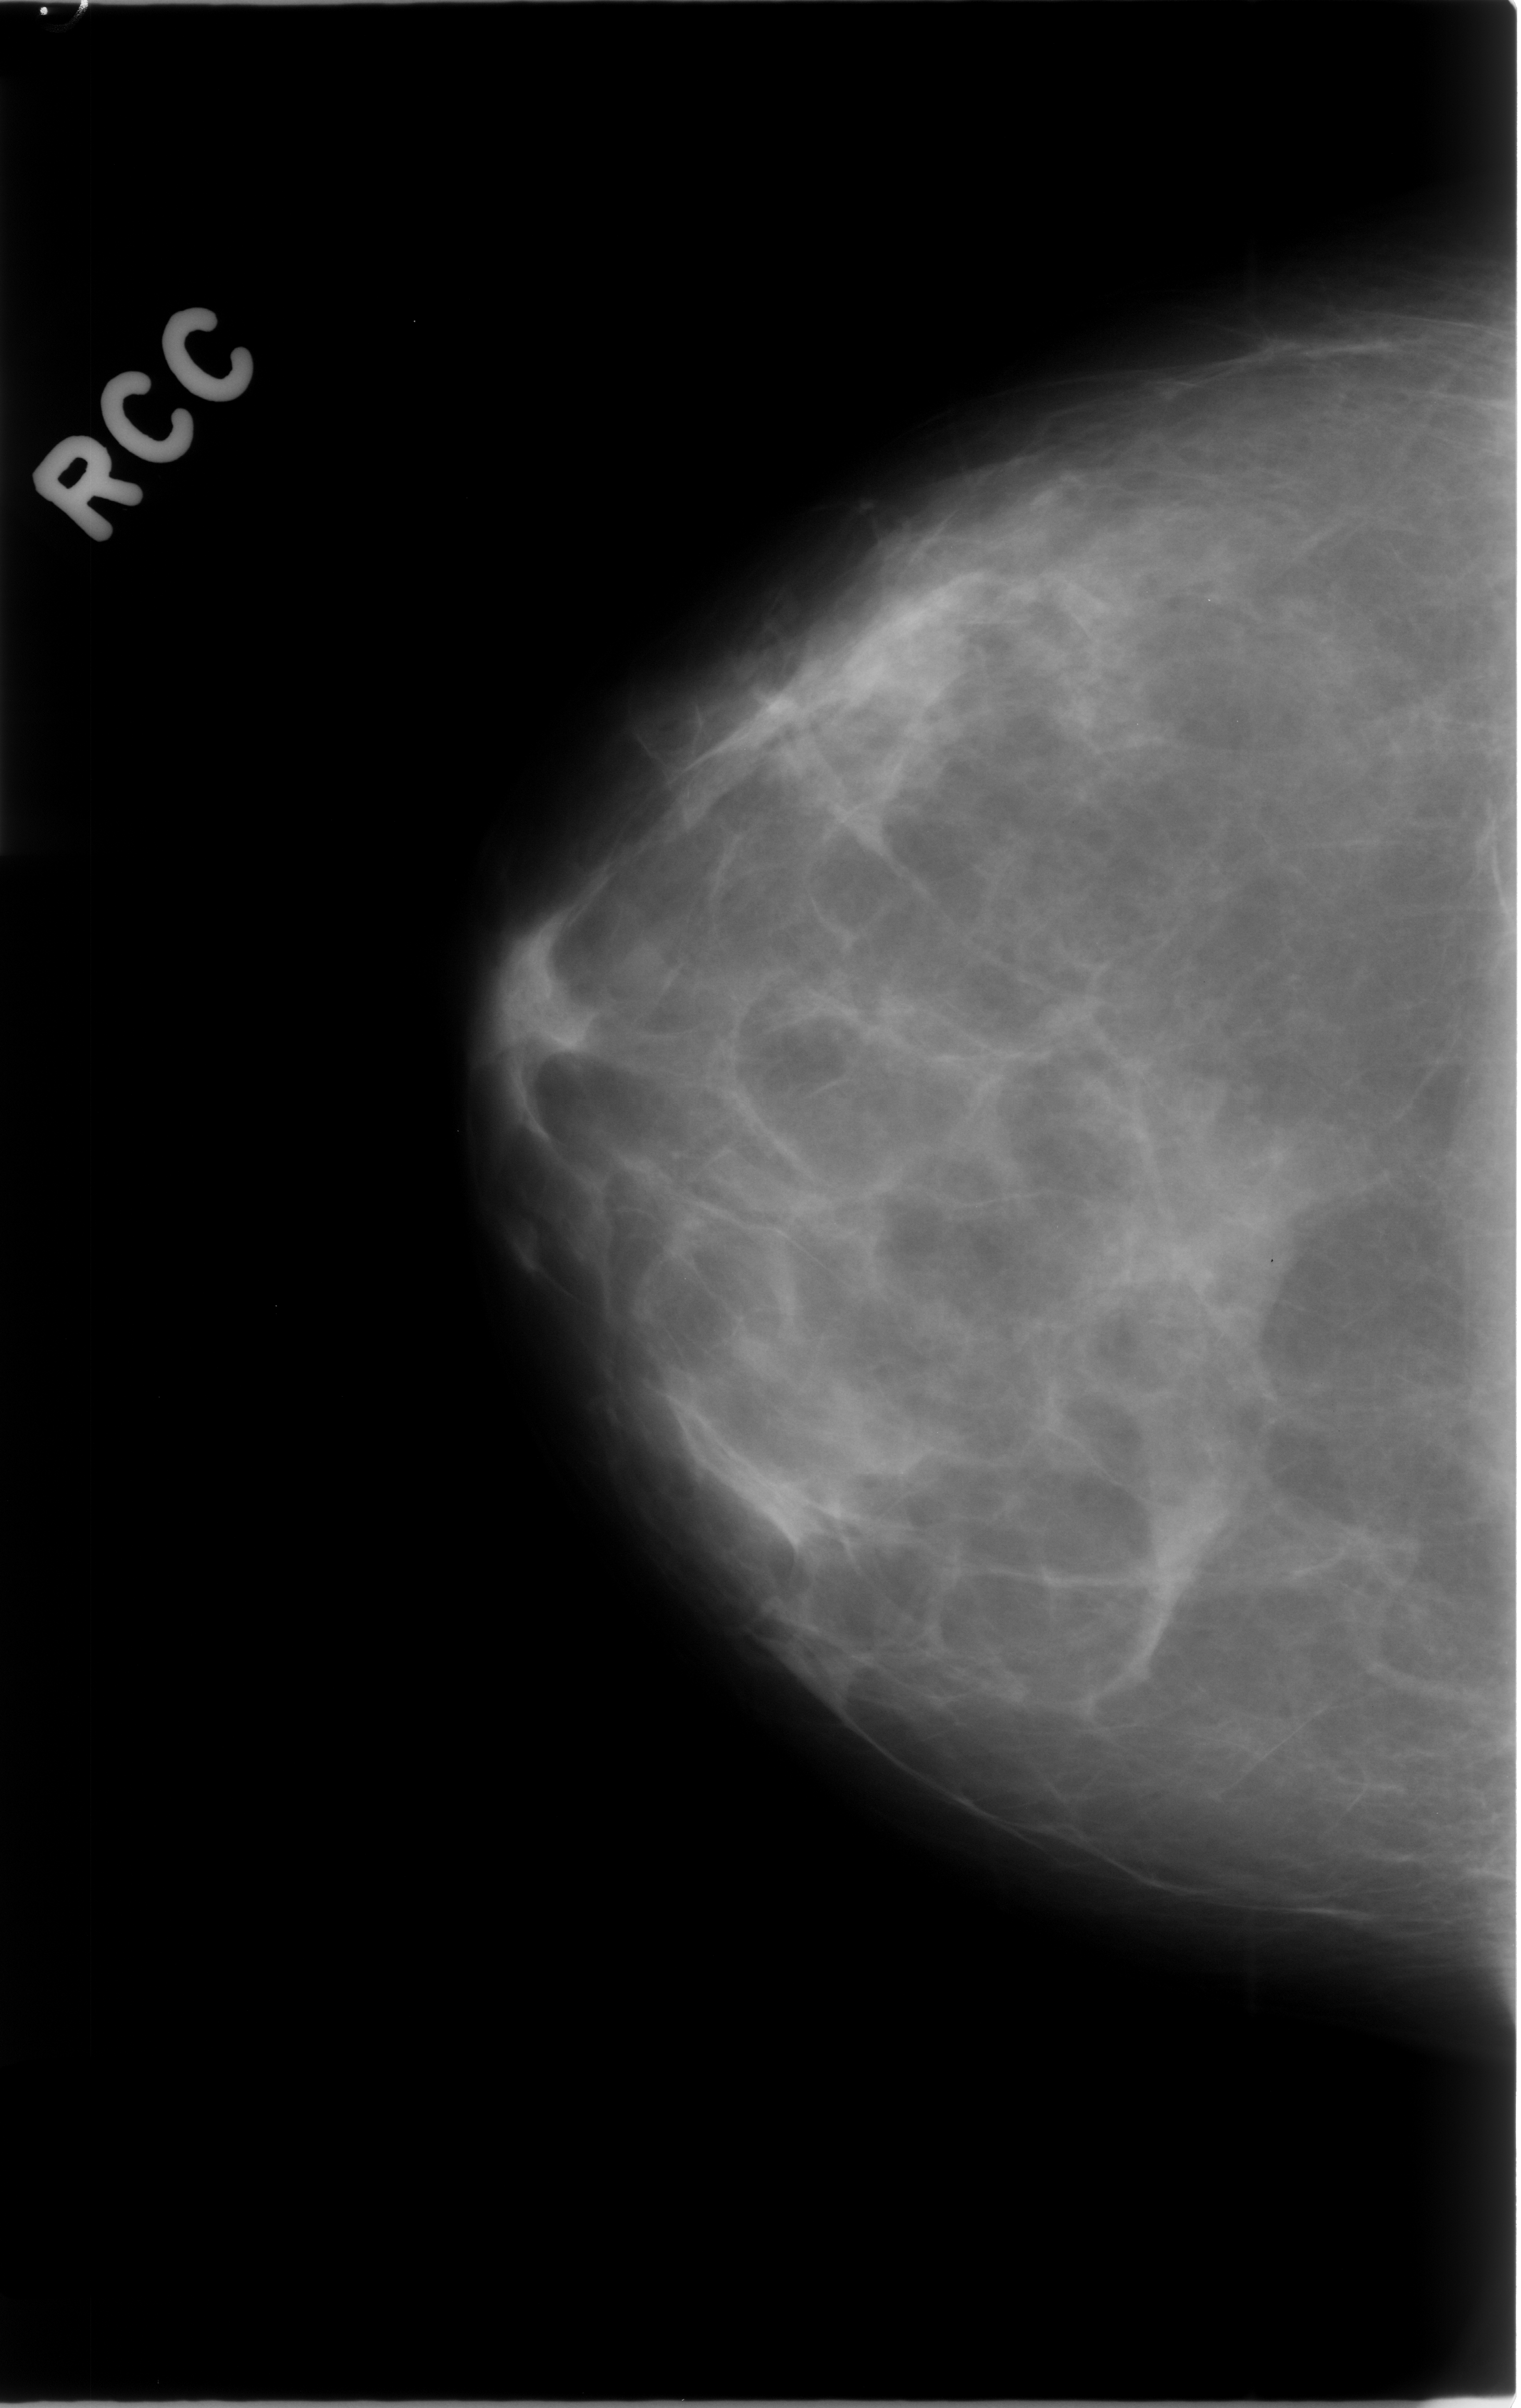
Digitized screen-film mammogram; right breast; craniocaudal (CC) view; breast composition: scattered fibroglandular densities (BI-RADS density category 2 of 4); 1521 × 2408 image matrix.
Marked abnormalities (boxes around the expert regions of interest):
- mass, shape asymmetric breast tissue, margins ill defined; BI-RADS assessment category 3; subtlety rating 5 on a 1 (subtle) to 5 (obvious) scale; outcome (as recorded, no biopsy): benign without callback (not worked up further): bounding box [x1, y1, x2, y2] px = [1073, 1115, 1293, 1383]